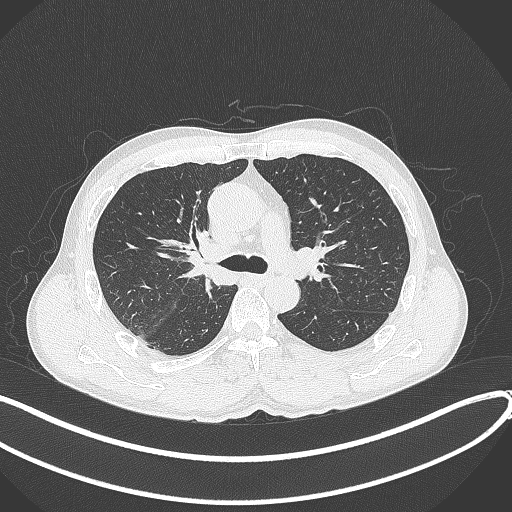
Chest CT, one axial slice; position 248 of 409 along the scan axis; reconstruction kernel B70f; 120 kVp; lung window (W 1500 / L -600 HU); 1 mm slice thickness; 512 × 512 image matrix, field of view 400 × 400 mm. Male patient, age 53 years. Case-level facts recorded for this patient, not image findings: clinical TNM (as recorded): T1b N0 M0.
Outlined on this slice (bounding box drawn by a radiologist):
- lung tumour (recorded histology: squamous cell carcinoma): bounding box (x1, y1, x2, y2) in pixels: (184, 232, 240, 291)